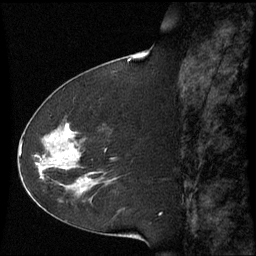
Breast MRI (dynamic contrast-enhanced), one sagittal slice. Slice 24 of 60 in the series (ordered by position). Dynamic contrast-enhanced series, image 2 of 3 at this slice position (ordered by acquisition). 1.5 T. TE 4.2 ms, TR 8.9 ms. 2.3 mm slice thickness. 256 × 256 image matrix, field of view 210 × 210 mm. Female patient, age 51 years. From the clinical record (not read from this slice): setting: breast cancer imaged before/during neoadjuvant chemotherapy; receptor status: HR-positive, HER2-negative.
Outlined on this slice (semi-automatic segmentation, software-assisted and operator-edited):
- analysis volume of interest (the breast-tissue region the enhancement analysis was run in; not a lesion): box from (x=50, y=125) to (x=116, y=187) px
- tumour enhancement mask (voxels above the 70 % enhancement threshold inside the analysis volume of interest): (x=51, y=125)–(x=88, y=183)